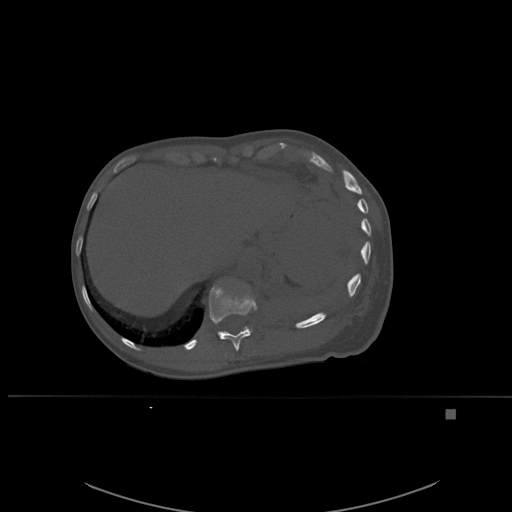
CT including the spine, one axial slice; position 296 of 537 along the scan axis; bone window (W 1800 / L 400 HU); 512 × 512 image matrix. Female patient, age 45 years. From the clinical record (not read from this slice): primary cancer: lung.
Outlined on this slice (semi-automatically segmented with operator editing):
- T11 vertebra: bounding box (x1, y1, x2, y2) in pixels: (209, 286, 257, 352)
- T12 vertebra: (216, 281, 252, 330)